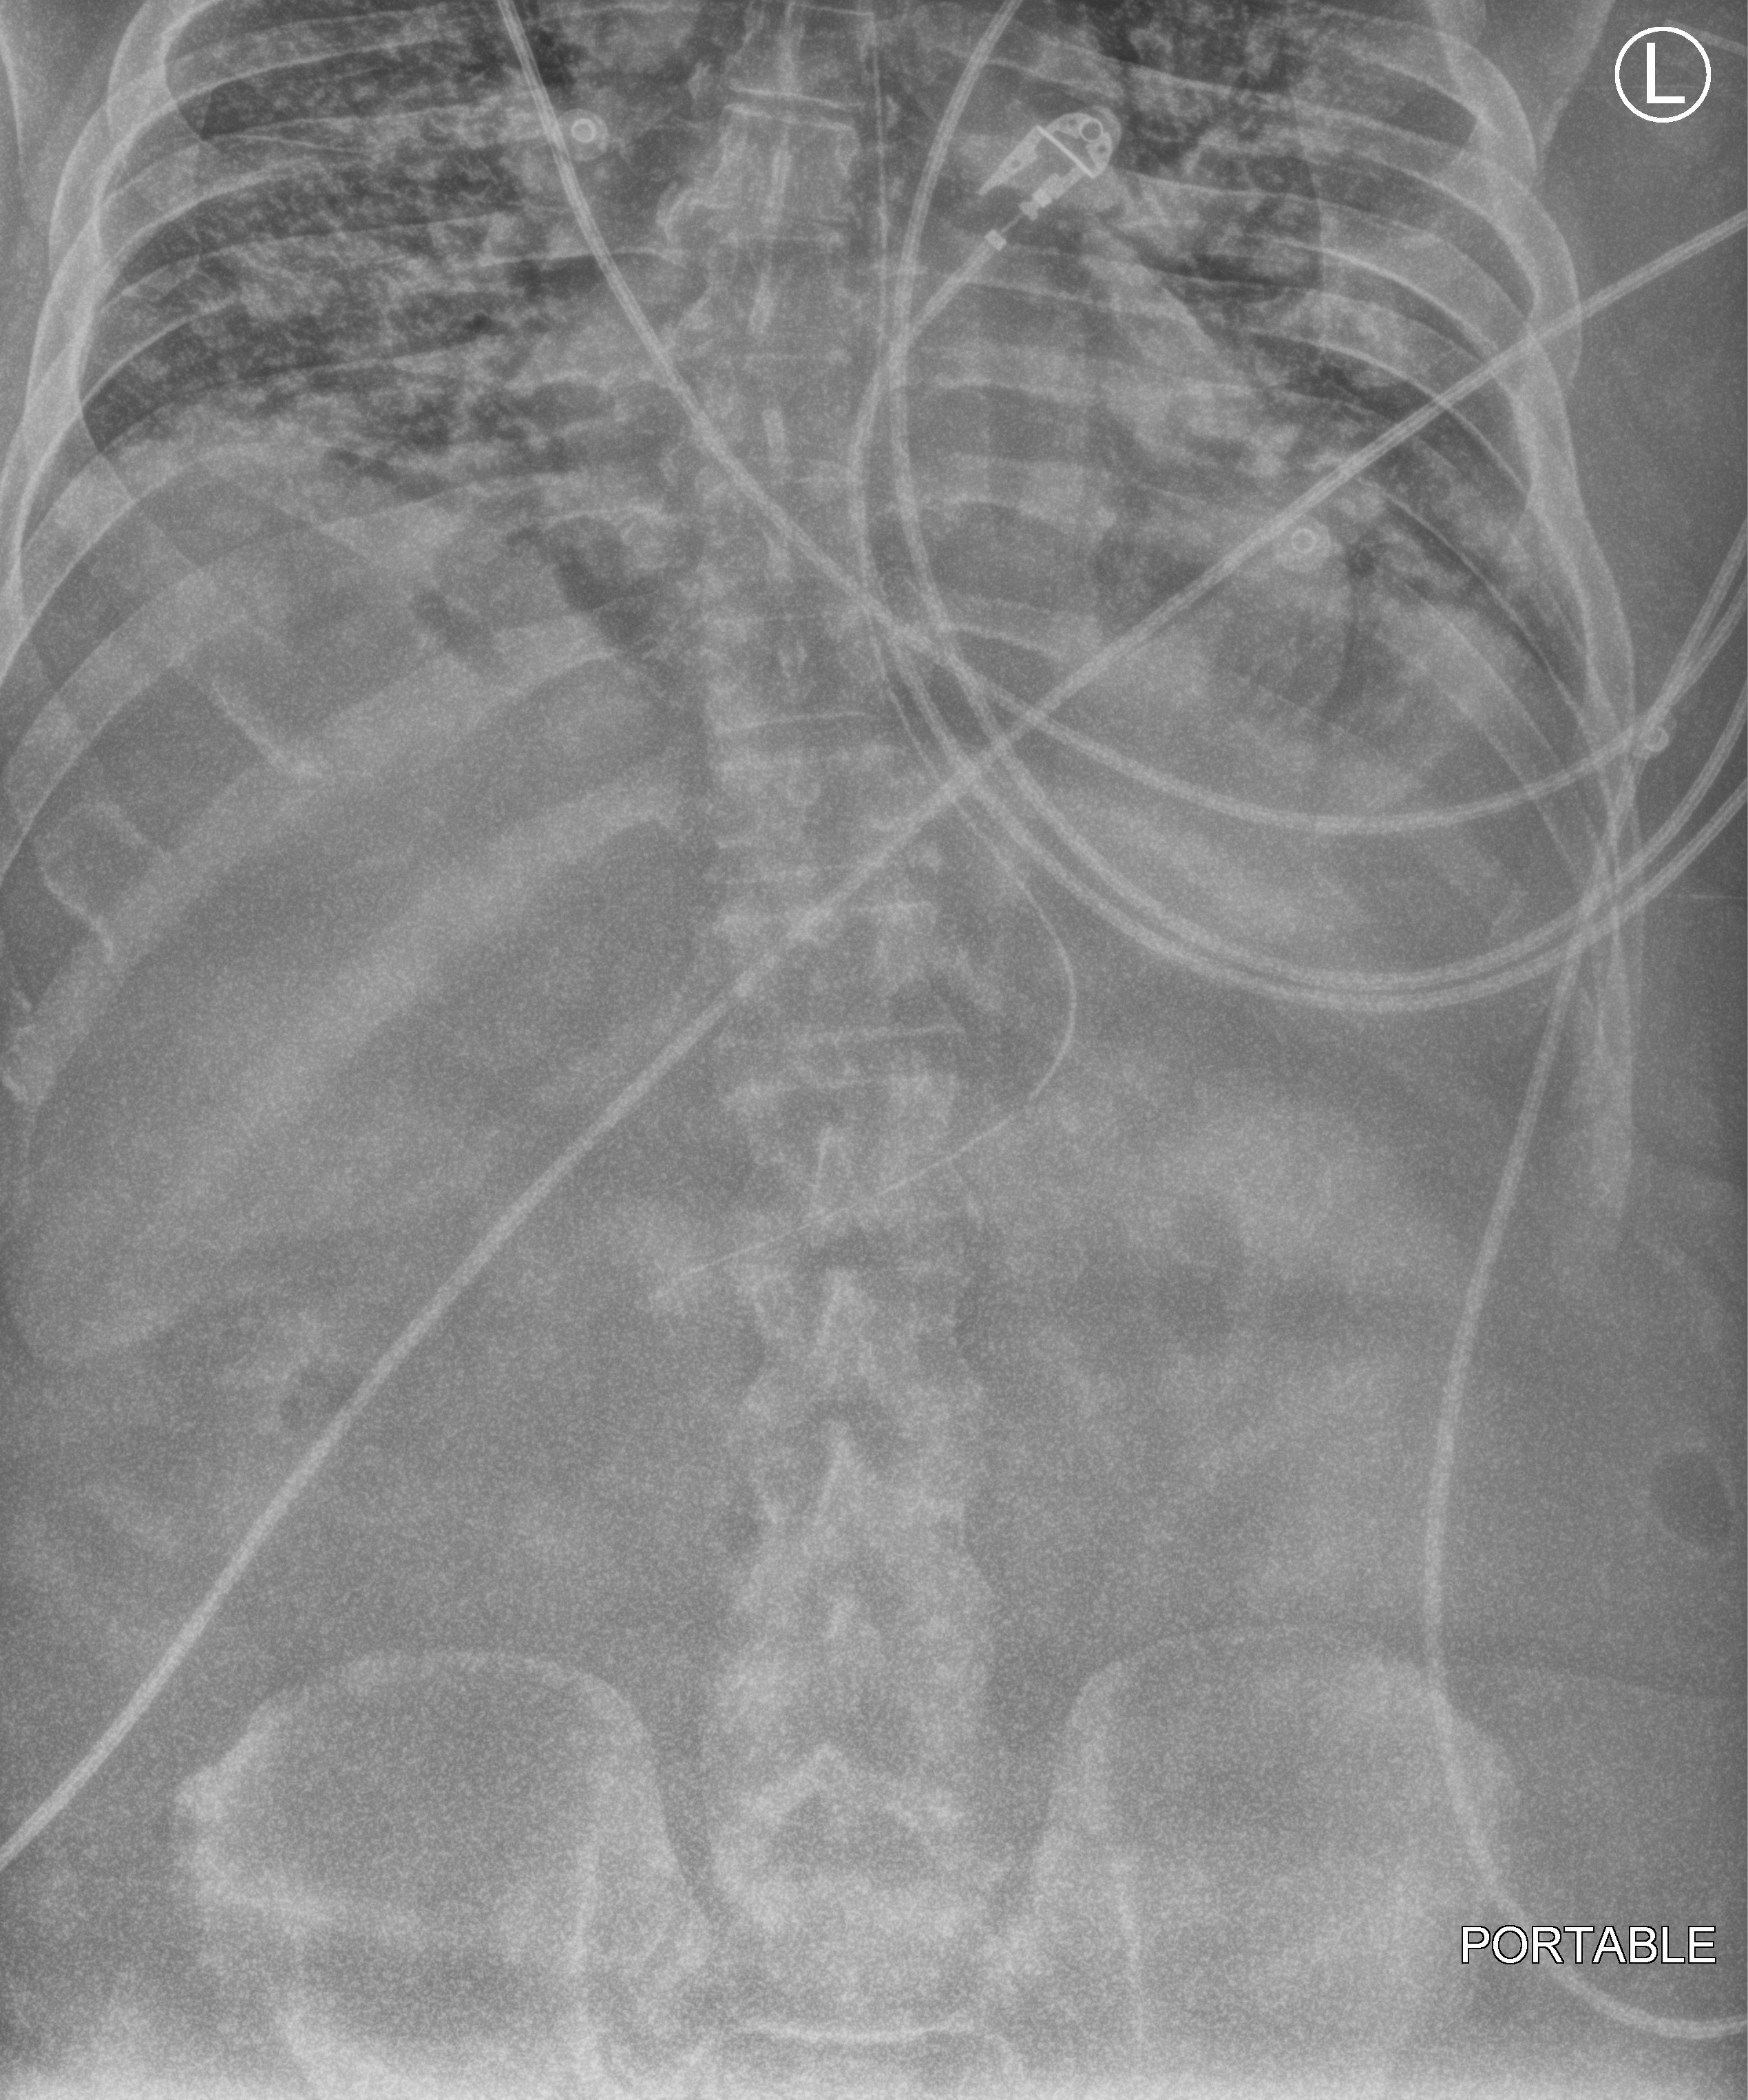
Portable abdomen radiograph. Male patient hospitalised with COVID-19, age 18–59 years.
Hospital-stay facts (about this admission, not read from this image; timing relative to this image not recorded):
- mechanically ventilated during this hospital stay: yes
- admitted to intensive care during this hospital stay: yes
- smoking status (admission record): never